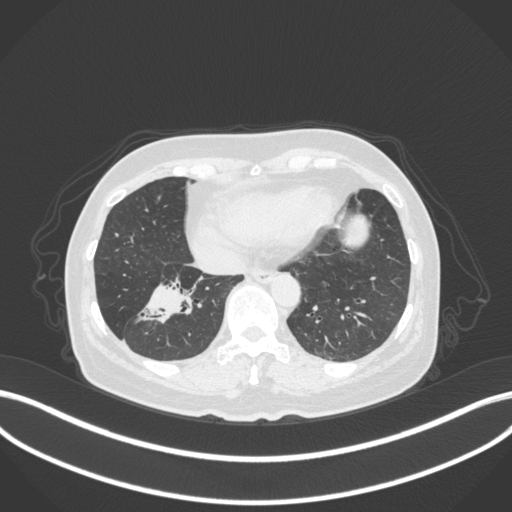
Chest CT, one axial slice. Position 117 of 429 along the scan axis. Reconstruction kernel B31f. 120 kVp. Lung window (W 1500 / L -600 HU). 1 mm slice thickness. 512 × 512 image matrix. Patient: female, 67 years. Case-level facts recorded for this patient, not image findings: clinical TNM (as recorded): T1c N1 M0.
Outlined on this slice (bounding box drawn by a radiologist):
- lung tumour (recorded histology: adenocarcinoma): bounding box <130,270,208,325> (left, top, right, bottom; pixels)